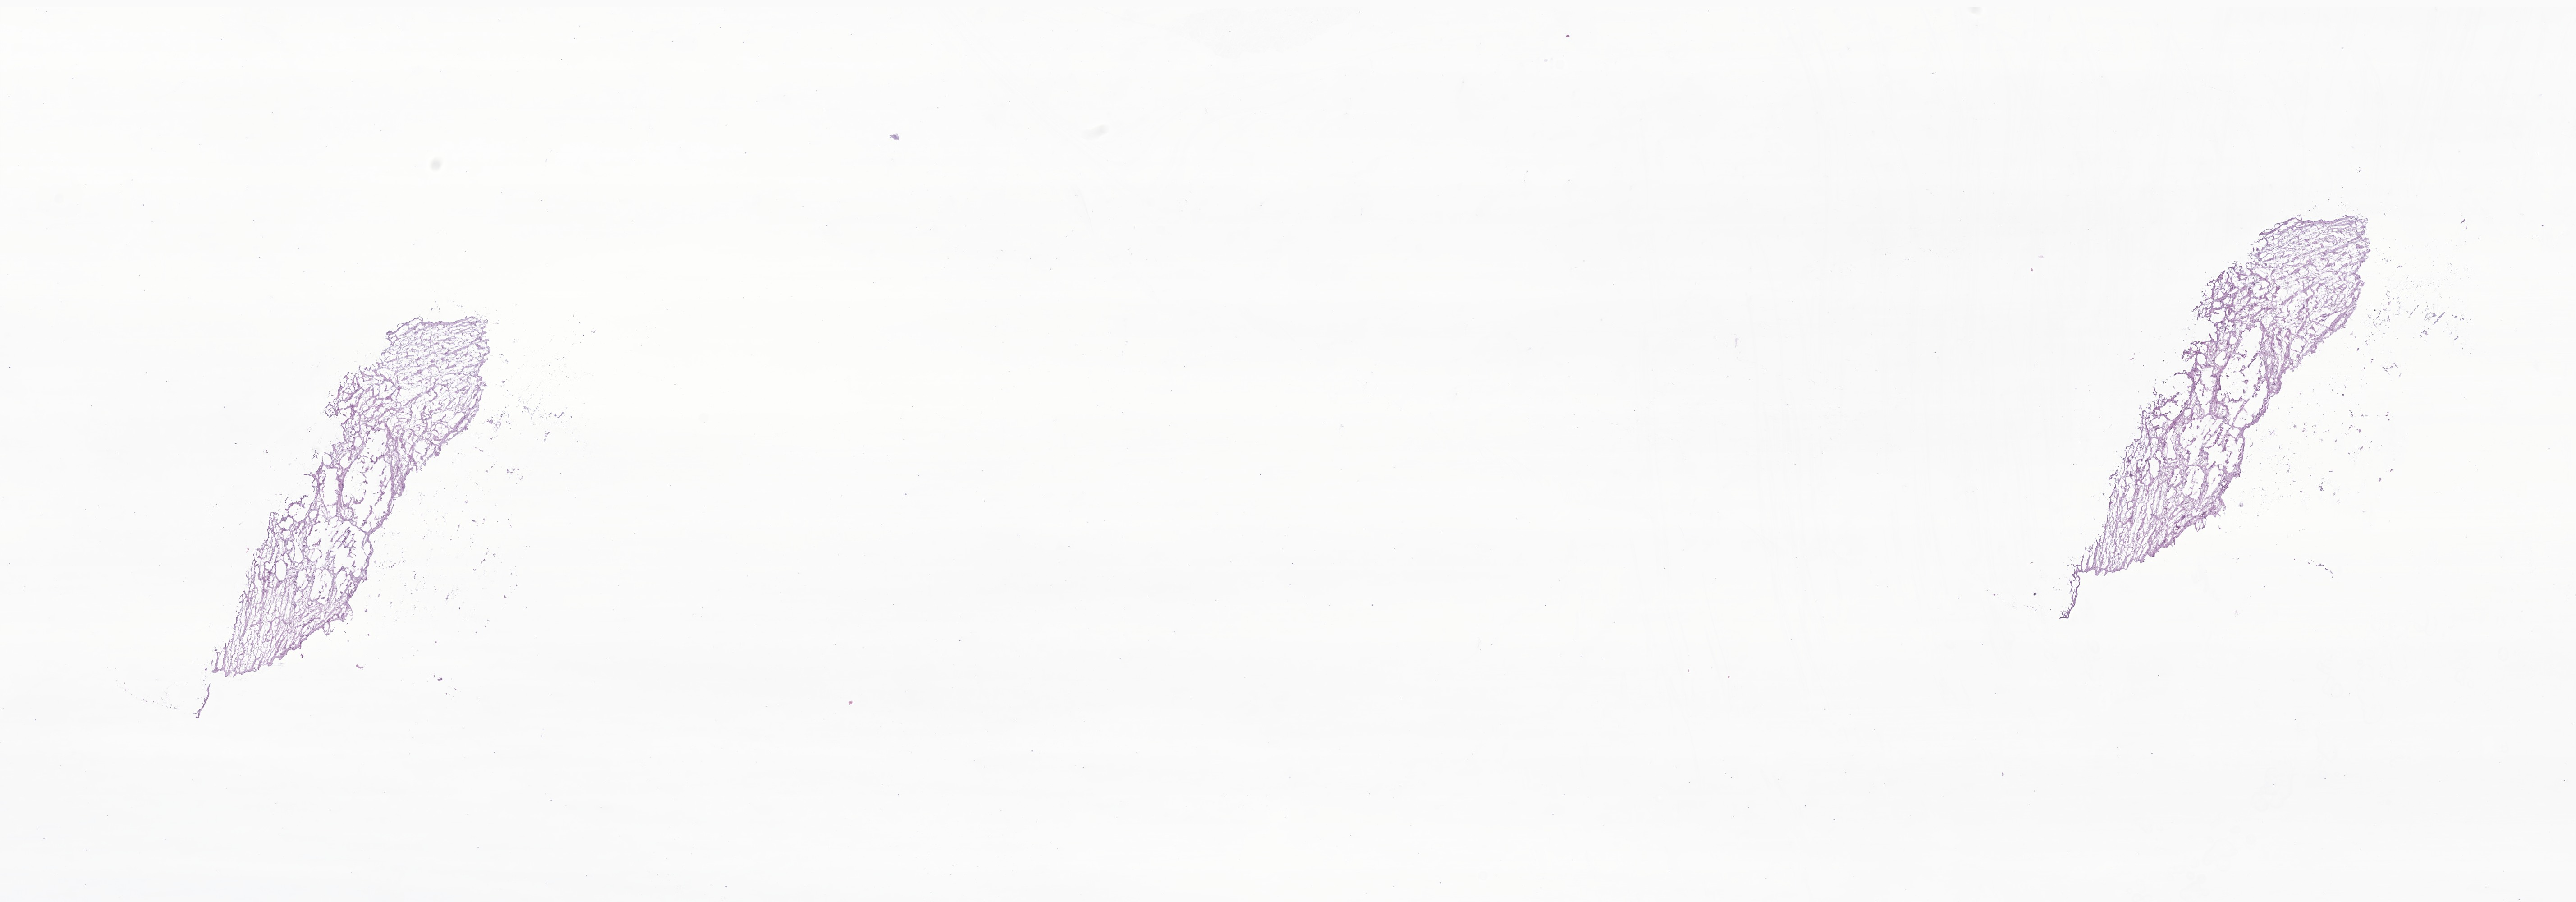
Haematoxylin and eosin whole-slide image of tumor tissue from the spinal cord, low-resolution overview of the scanned area, about 24.1 x 8.4 mm, cryosection (OCT / tissue freezing medium). Male patient, age 128 months (10 years 8 months).
Diagnosis: Ganglioneuroblastoma.